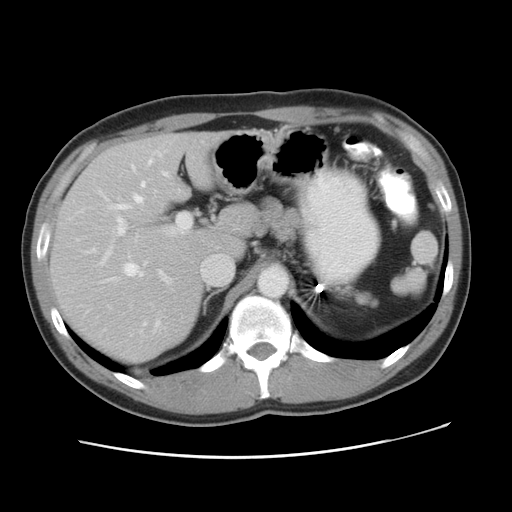
Contrast-enhanced abdominal CT, one axial slice; position 32 of 49 along the scan axis; reconstruction kernel STANDARD; 120 kVp; intravenous contrast given; soft-tissue window (W 400 / L 40 HU); 5 mm slice thickness; 512 × 512 image matrix, field of view 363 × 363 mm. Male patient, age 41 years. Case-level facts recorded for this patient, not image findings: diagnosis: colorectal cancer liver metastases, imaged before liver resection; multiple liver metastases: yes; largest metastasis: 0.7 cm; chemotherapy before resection: yes.
Annotated regions visible in this slice (manually delineated by an expert):
- hepatic veins: bounding box <99,157,232,284> (left, top, right, bottom; pixels)
- liver: <50,132,245,363>
- planned liver remnant (the part of the liver to remain after resection): <101,132,245,258>
- portal vein (with intrahepatic branches): <89,213,192,325>